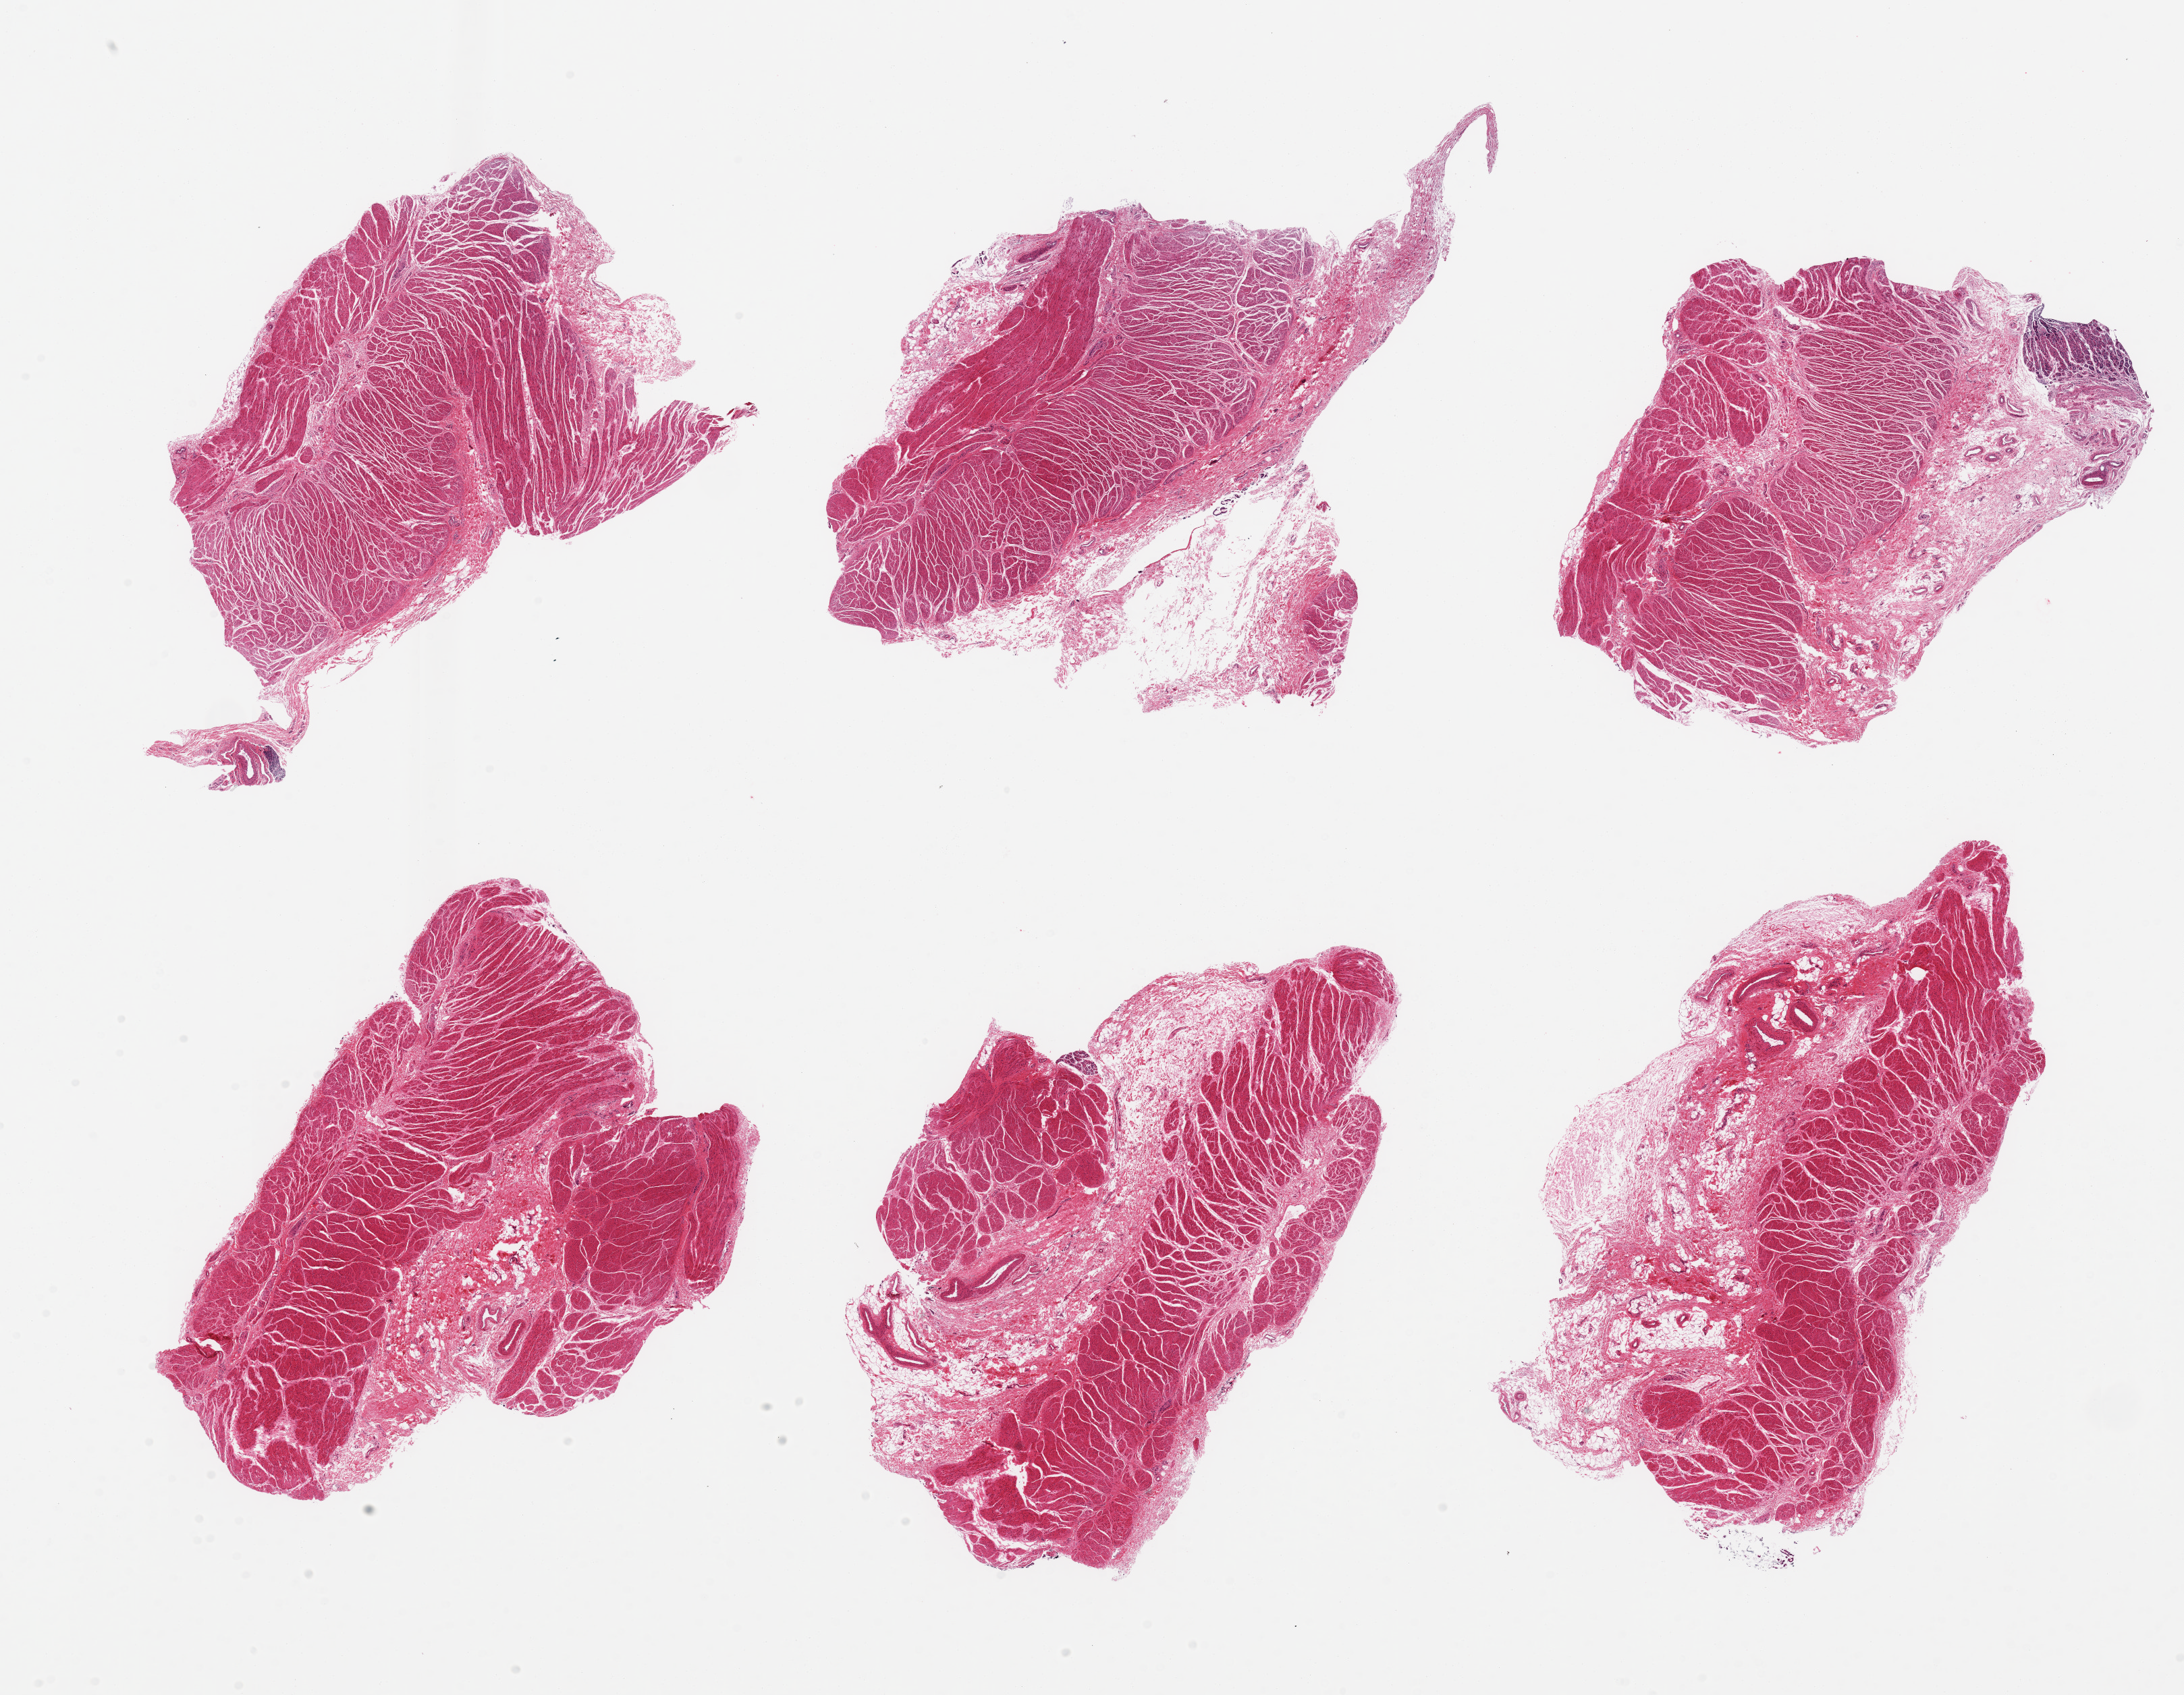
Whole-slide image, H&E stain, brightfield, low-resolution overview of the scanned area, about 25.6 x 19.9 mm (acquisition: 20x scan); PAXgene-fixed paraffin-embedded (PFPE) section; section of gastroesophageal junction (target tissue); tissue donor sample. Male donor.
Review note (as recorded): 6 pieces, confirmed target muscularis. Adherent rim of serosa up to ~1.5mm.